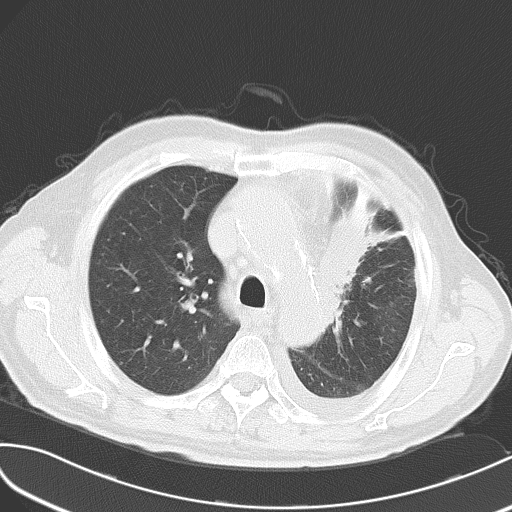
Chest CT, one axial slice; slice 40 of 54 in the series (ordered by position); 120 kVp; lung window (W 1500 / L -600 HU); 512 × 512 image matrix, field of view 353 × 353 mm. Patient: male, 70 years. From the clinical record (not read from this slice): clinical TNM (as recorded): T2 N1 M3; histopathological grade: G3.
Outlined on this slice (bounding box drawn by a radiologist):
- lung tumour (recorded histology: small cell carcinoma): bounding box <323,185,384,295> (left, top, right, bottom; pixels)